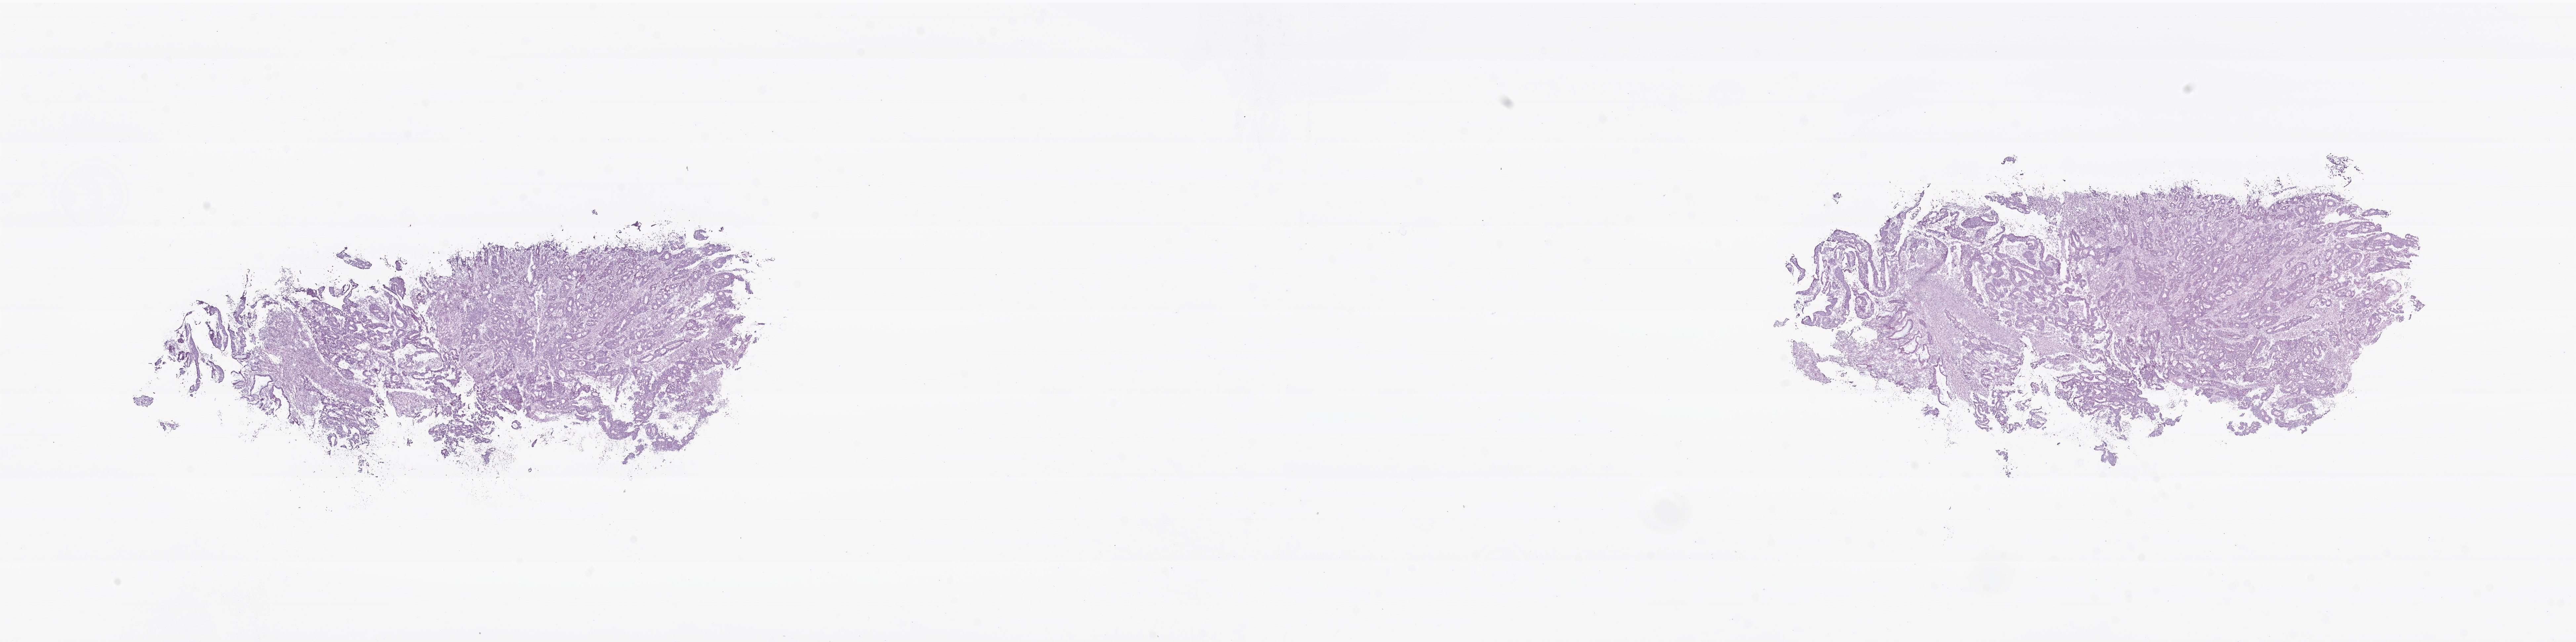
Whole-slide image, H&E stain of tumor tissue from the colon — shown as a low-resolution overview of the whole scanned area (about 32.8 x 8.2 mm); cryosection (OCT / tissue freezing medium). Patient: male, age 171 months (14 years 3 months).
Diagnosis: Adenocarcinoma, NOS.